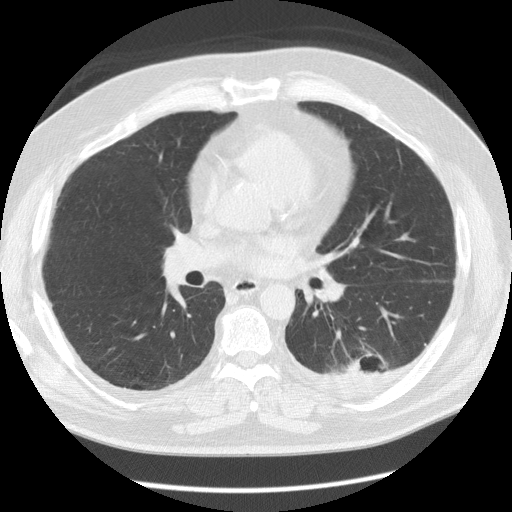
Low-dose screening chest CT, one axial slice; slice 68 of 126 in the series (ordered by position); 120 kVp; lung window (W 1500 / L -600 HU); 2.5 mm slice thickness; 512 × 512 image matrix, field of view 370 × 370 mm.
Outlined on this slice (outlined manually by an expert reader):
- lesion 1 (tumor, lower lobe of left lung): bounding box [x1, y1, x2, y2] px = [345, 356, 382, 374]